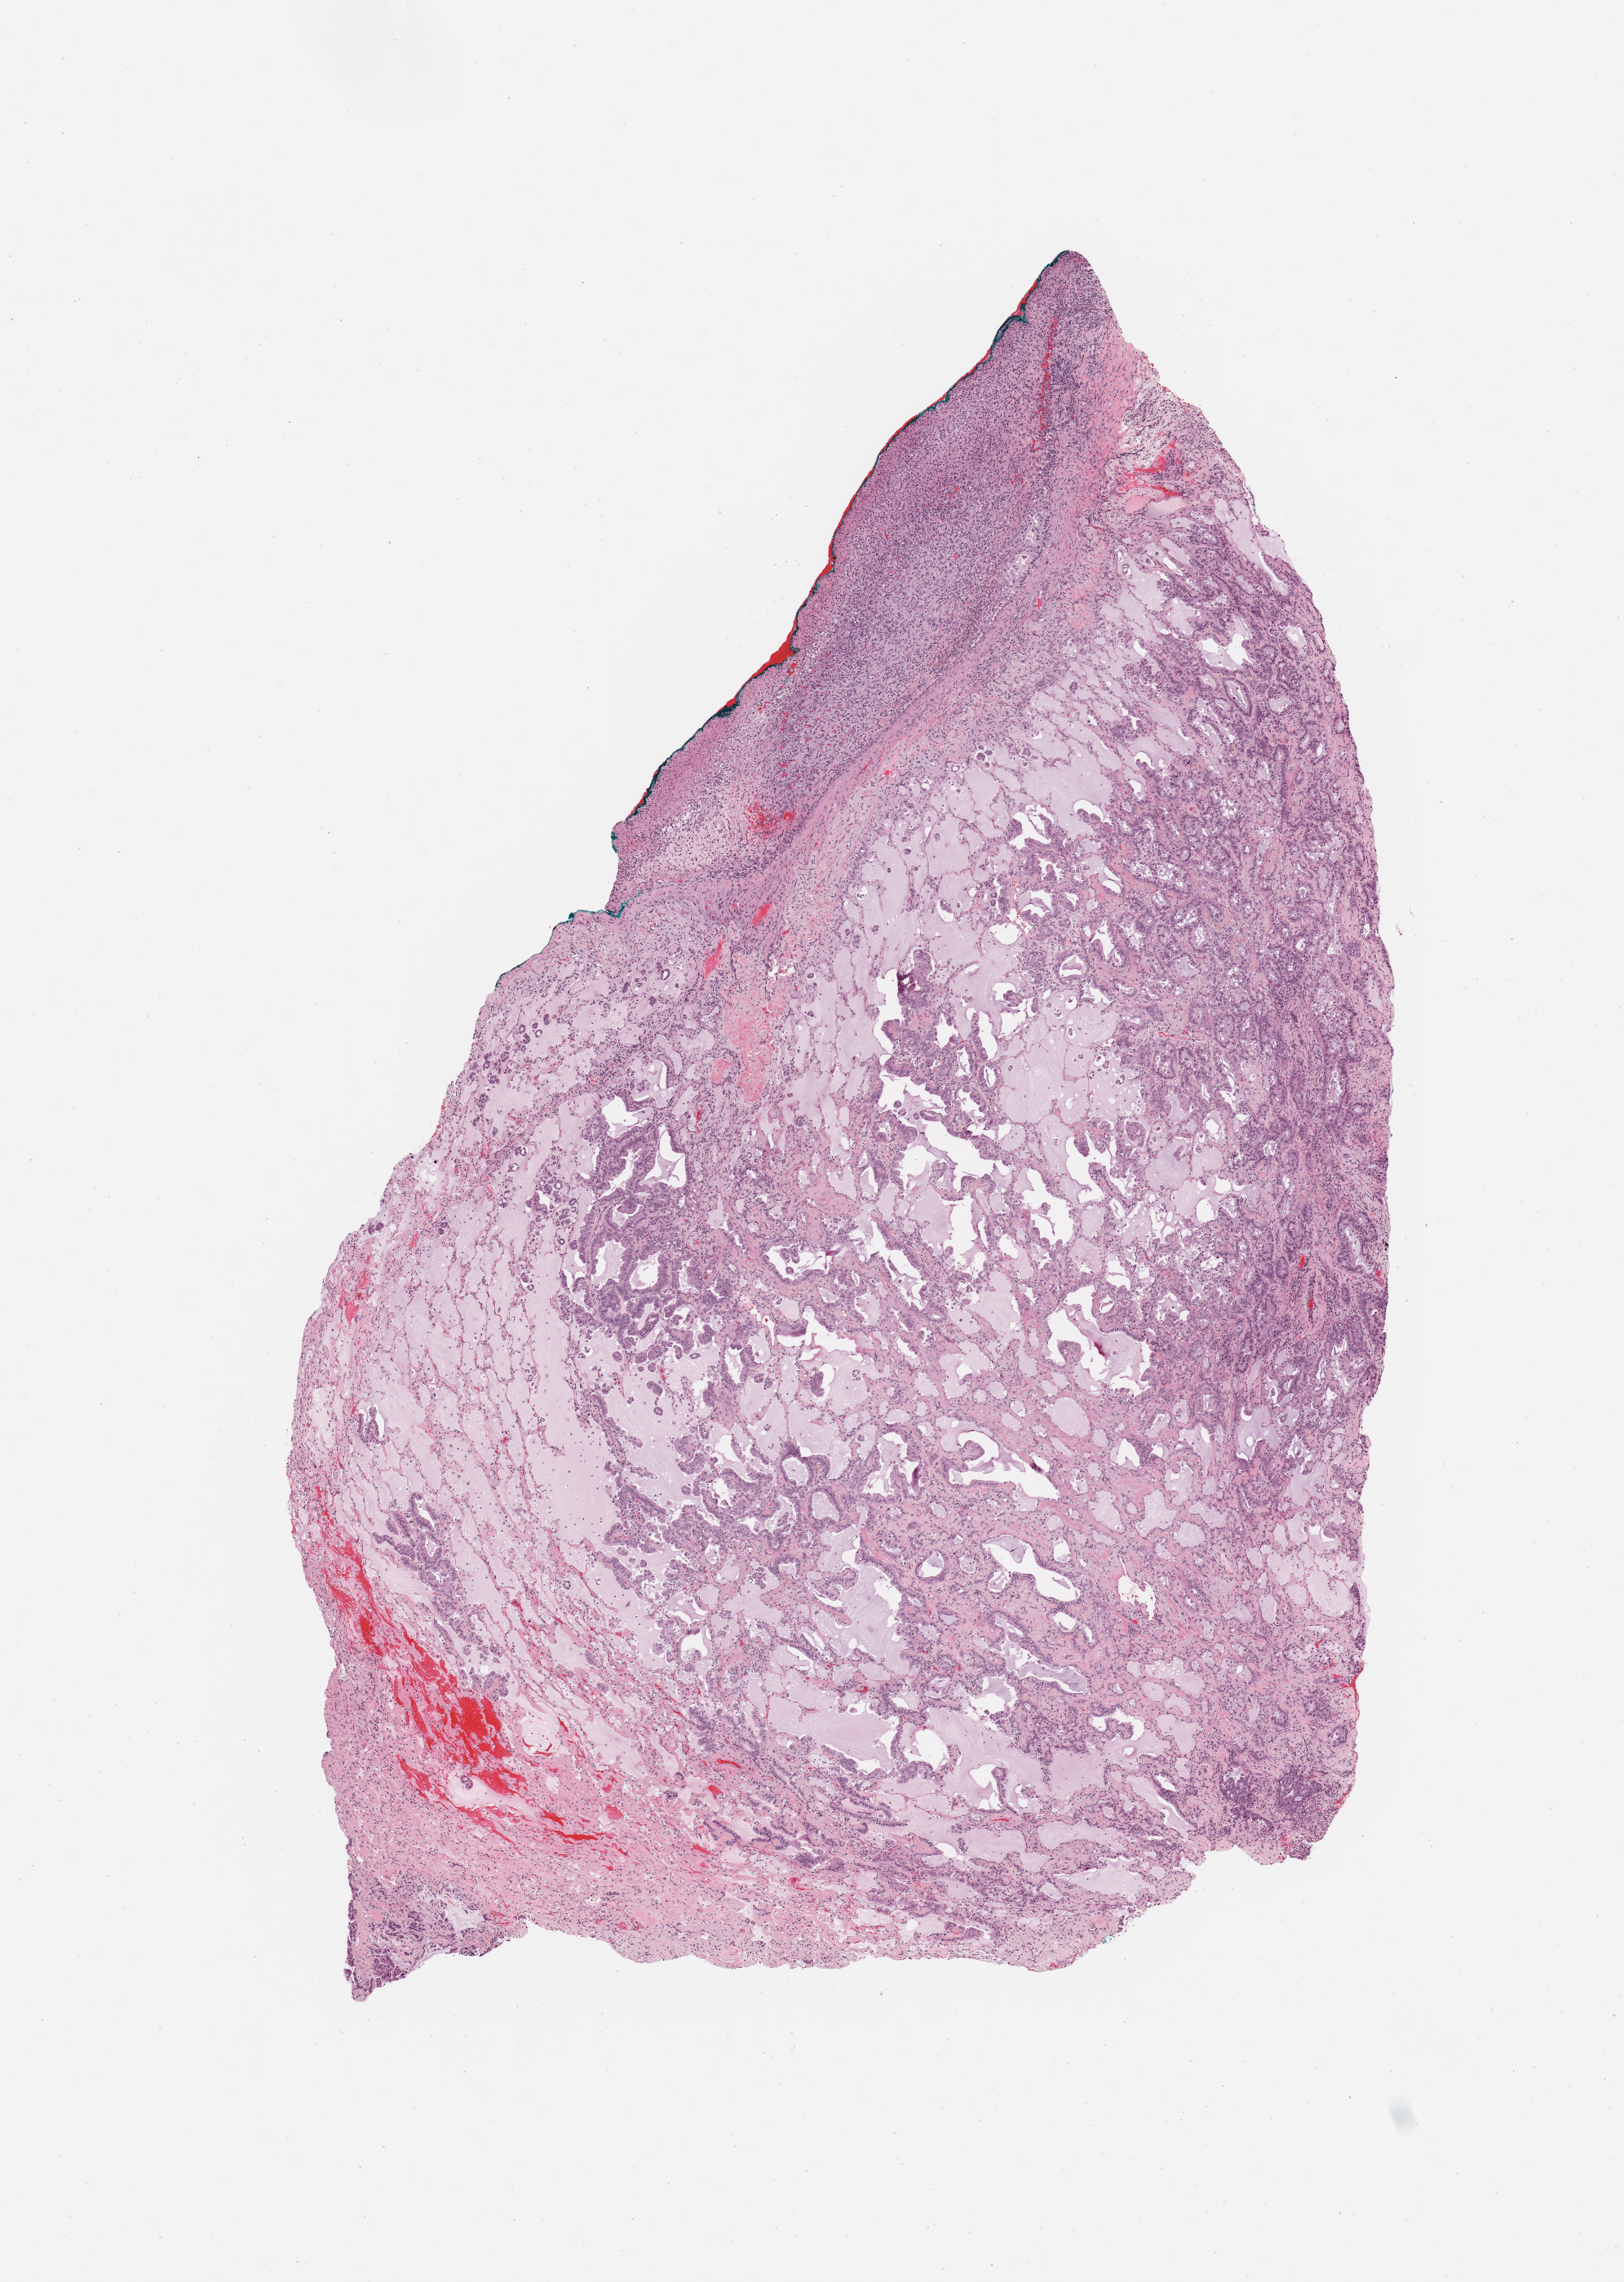
Whole-slide histology image, Hematoxylin and eosin (H&E) stained — low-resolution overview of the scanned area, about 7.9 x 11.1 mm (slide scanned at 20x); tumour tissue sample, lung. 60-year-old female patient. Histologic grade: G3 (poorly differentiated).
* primary tumour site (as recorded): right upper lobe
* diagnosis: Adenocarcinoma, NOS
* AJCC pathologic stage: IIA